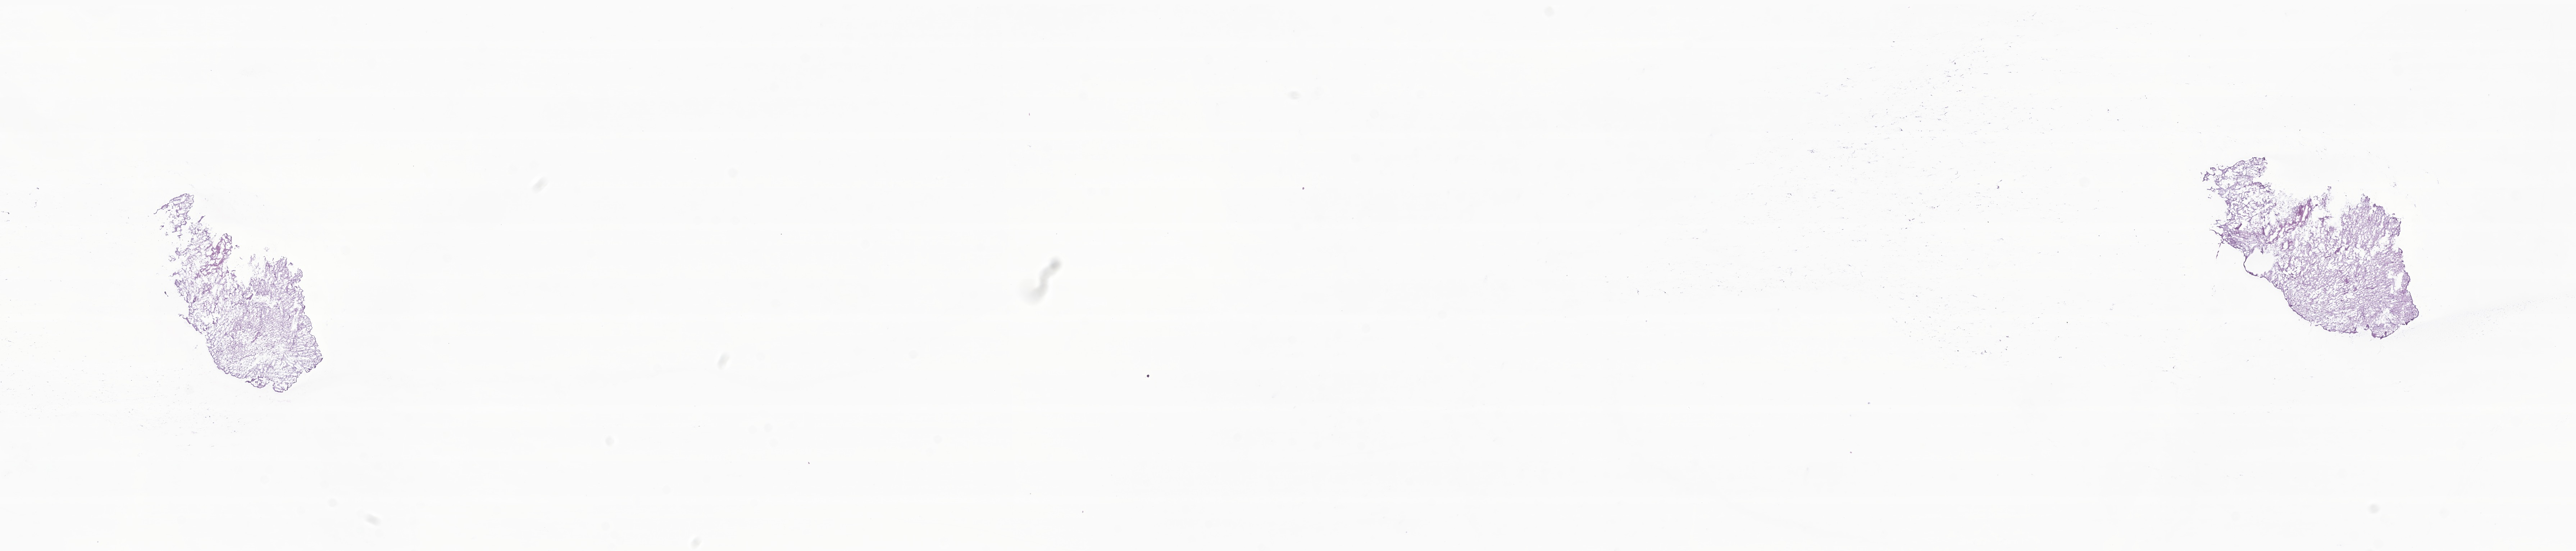
Haematoxylin and eosin whole-slide image of tumor tissue from the brain — shown as a low-resolution overview of the whole scanned area (about 30.2 x 6.5 mm), cryosection (OCT / tissue freezing medium). Patient: female, age 44 months.
• diagnosis: Pilocytic astrocytoma